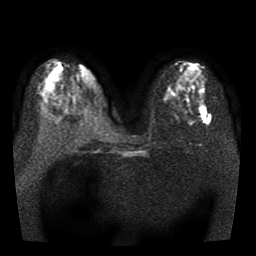
Breast MRI, one axial slice. Slice 16 of 41 in the series (ordered by position). Diffusion-weighted series; image 2 of 3 stored at this slice position (different b-values; order by instance number). 1.5 T. 5 mm slice thickness. 256 × 256 image matrix, field of view 330 × 330 mm. Female patient.
Outlined on this slice (manually delineated by an expert):
- tumour on diffusion-weighted imaging: bounding box (x1, y1, x2, y2) in pixels: (200, 107, 210, 123)